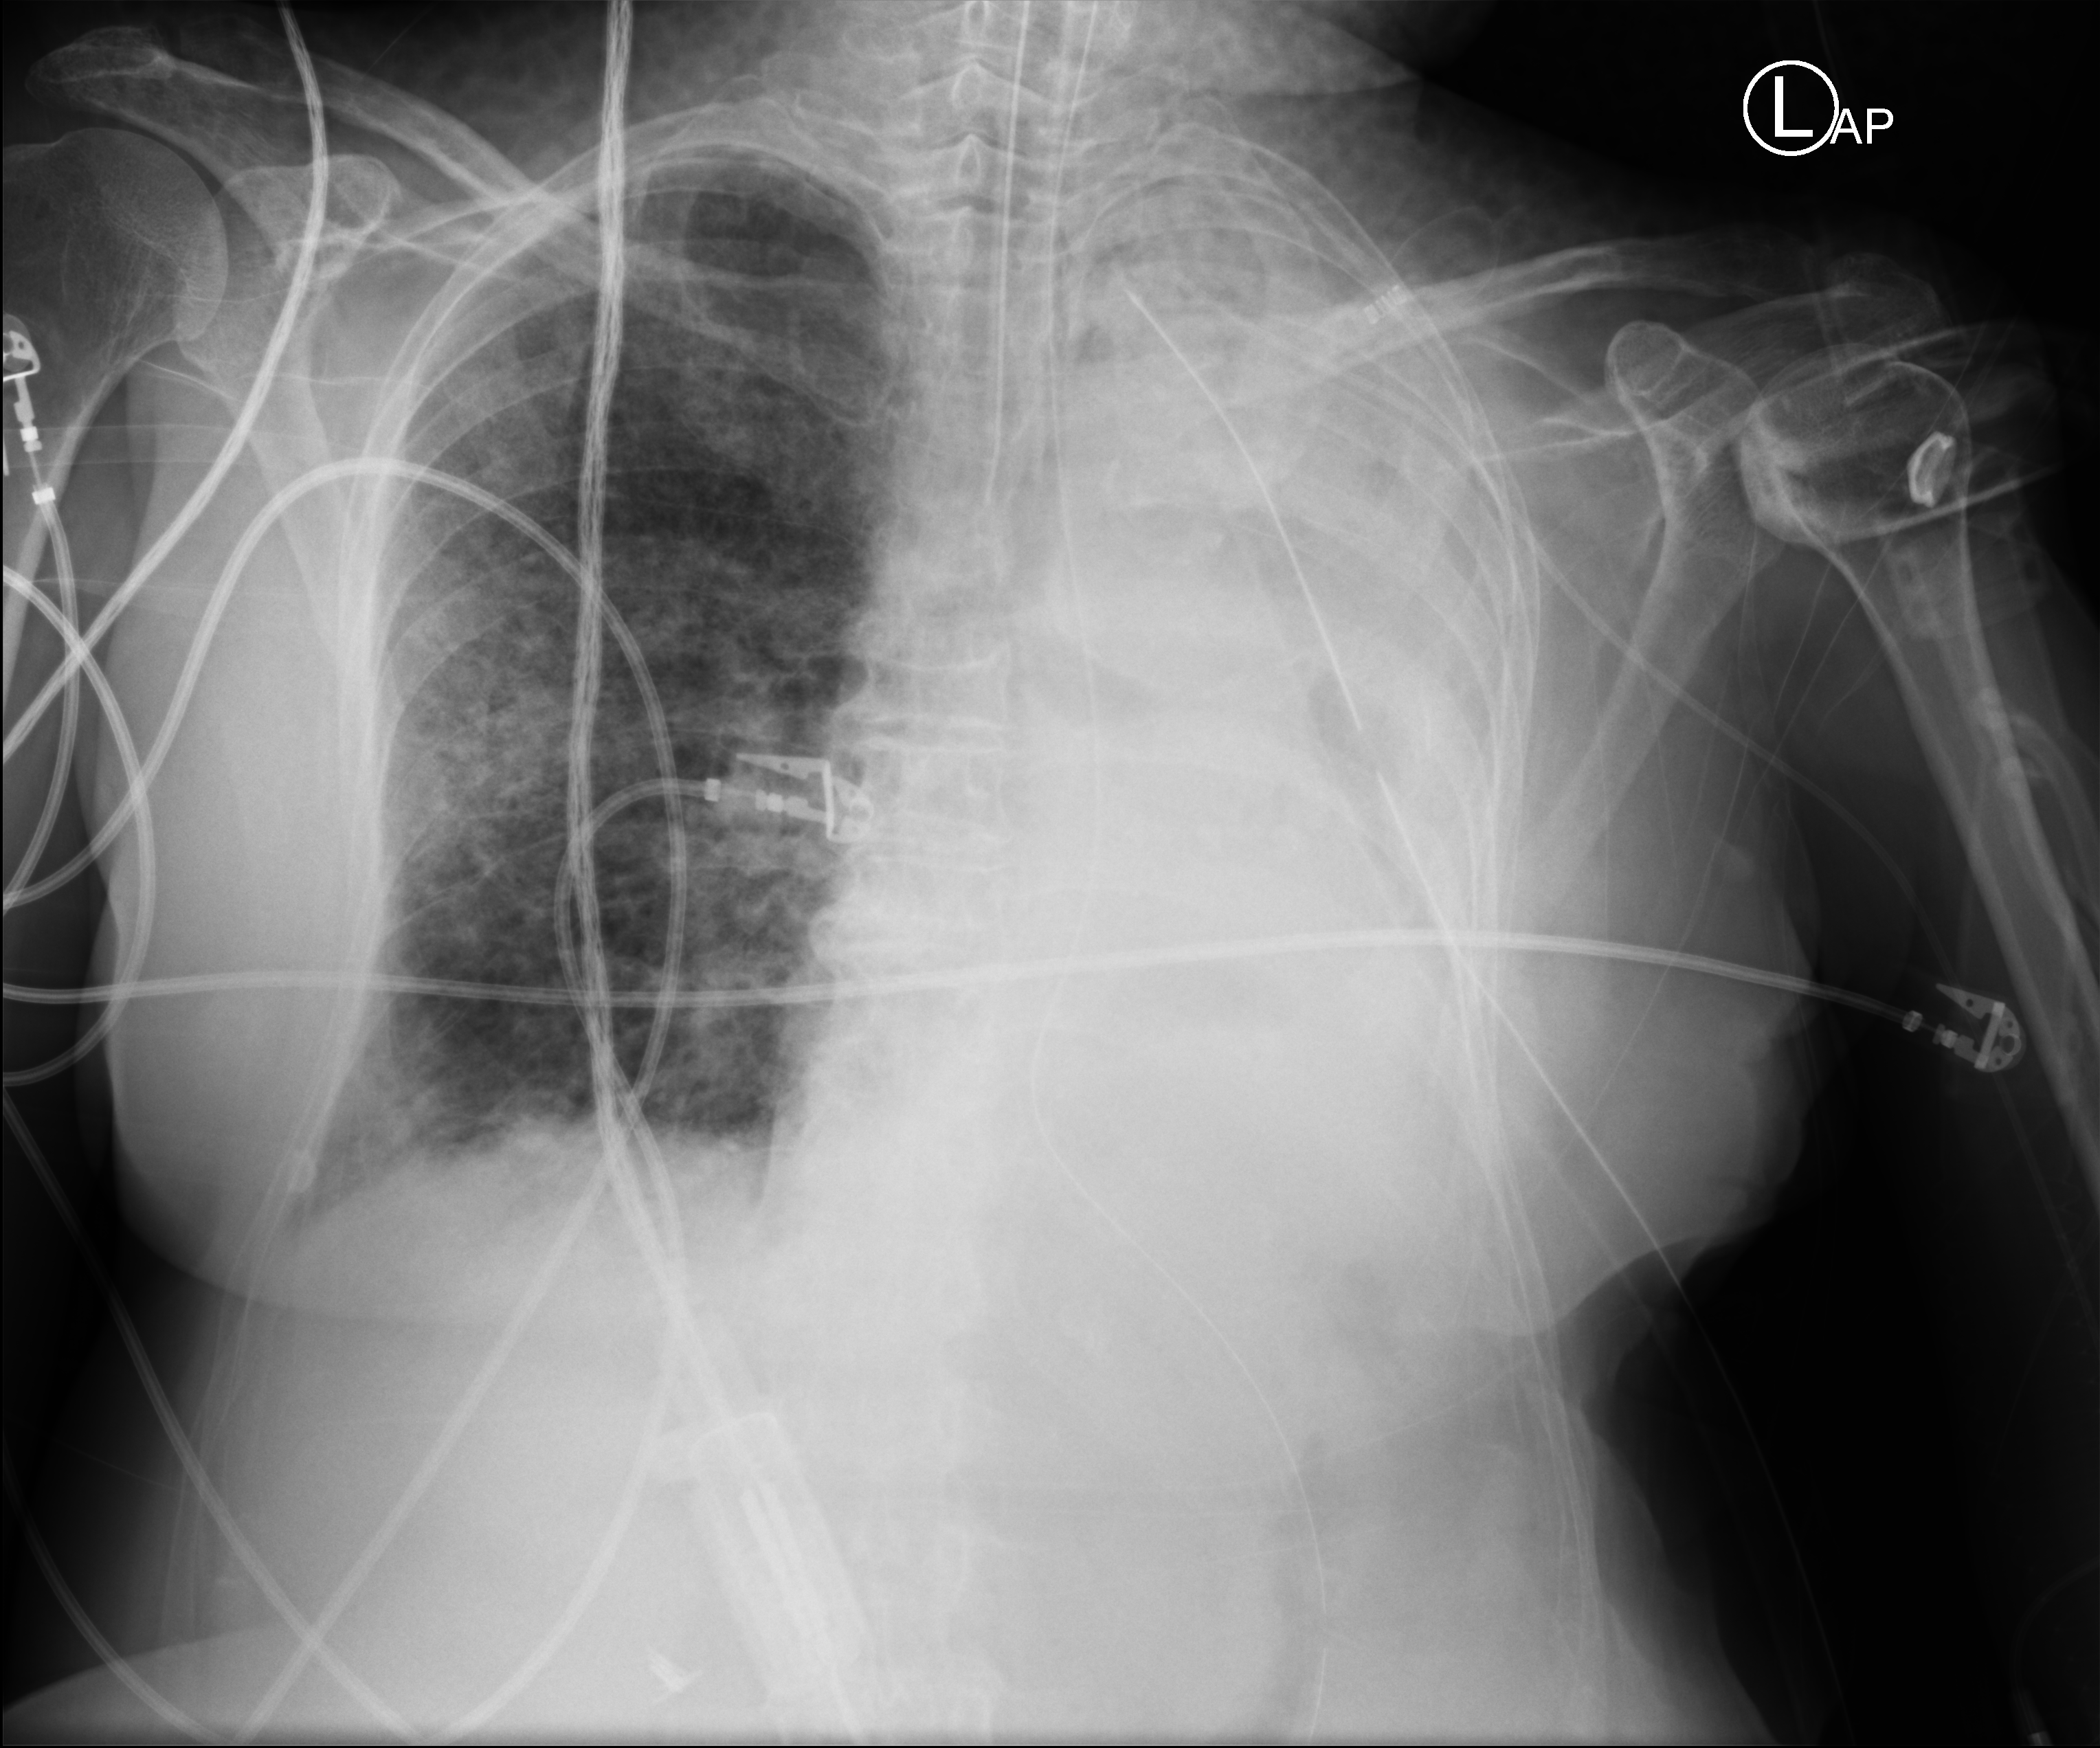
Bedside chest radiograph (computed radiography); anteroposterior (AP) projection. Patient hospitalised with COVID-19; female, aged 75–90 years.
Admission-level facts for this patient (not findings on this image; timing relative to this image not recorded): chronic kidney disease (admission record): no; mechanically ventilated during this hospital stay: yes.